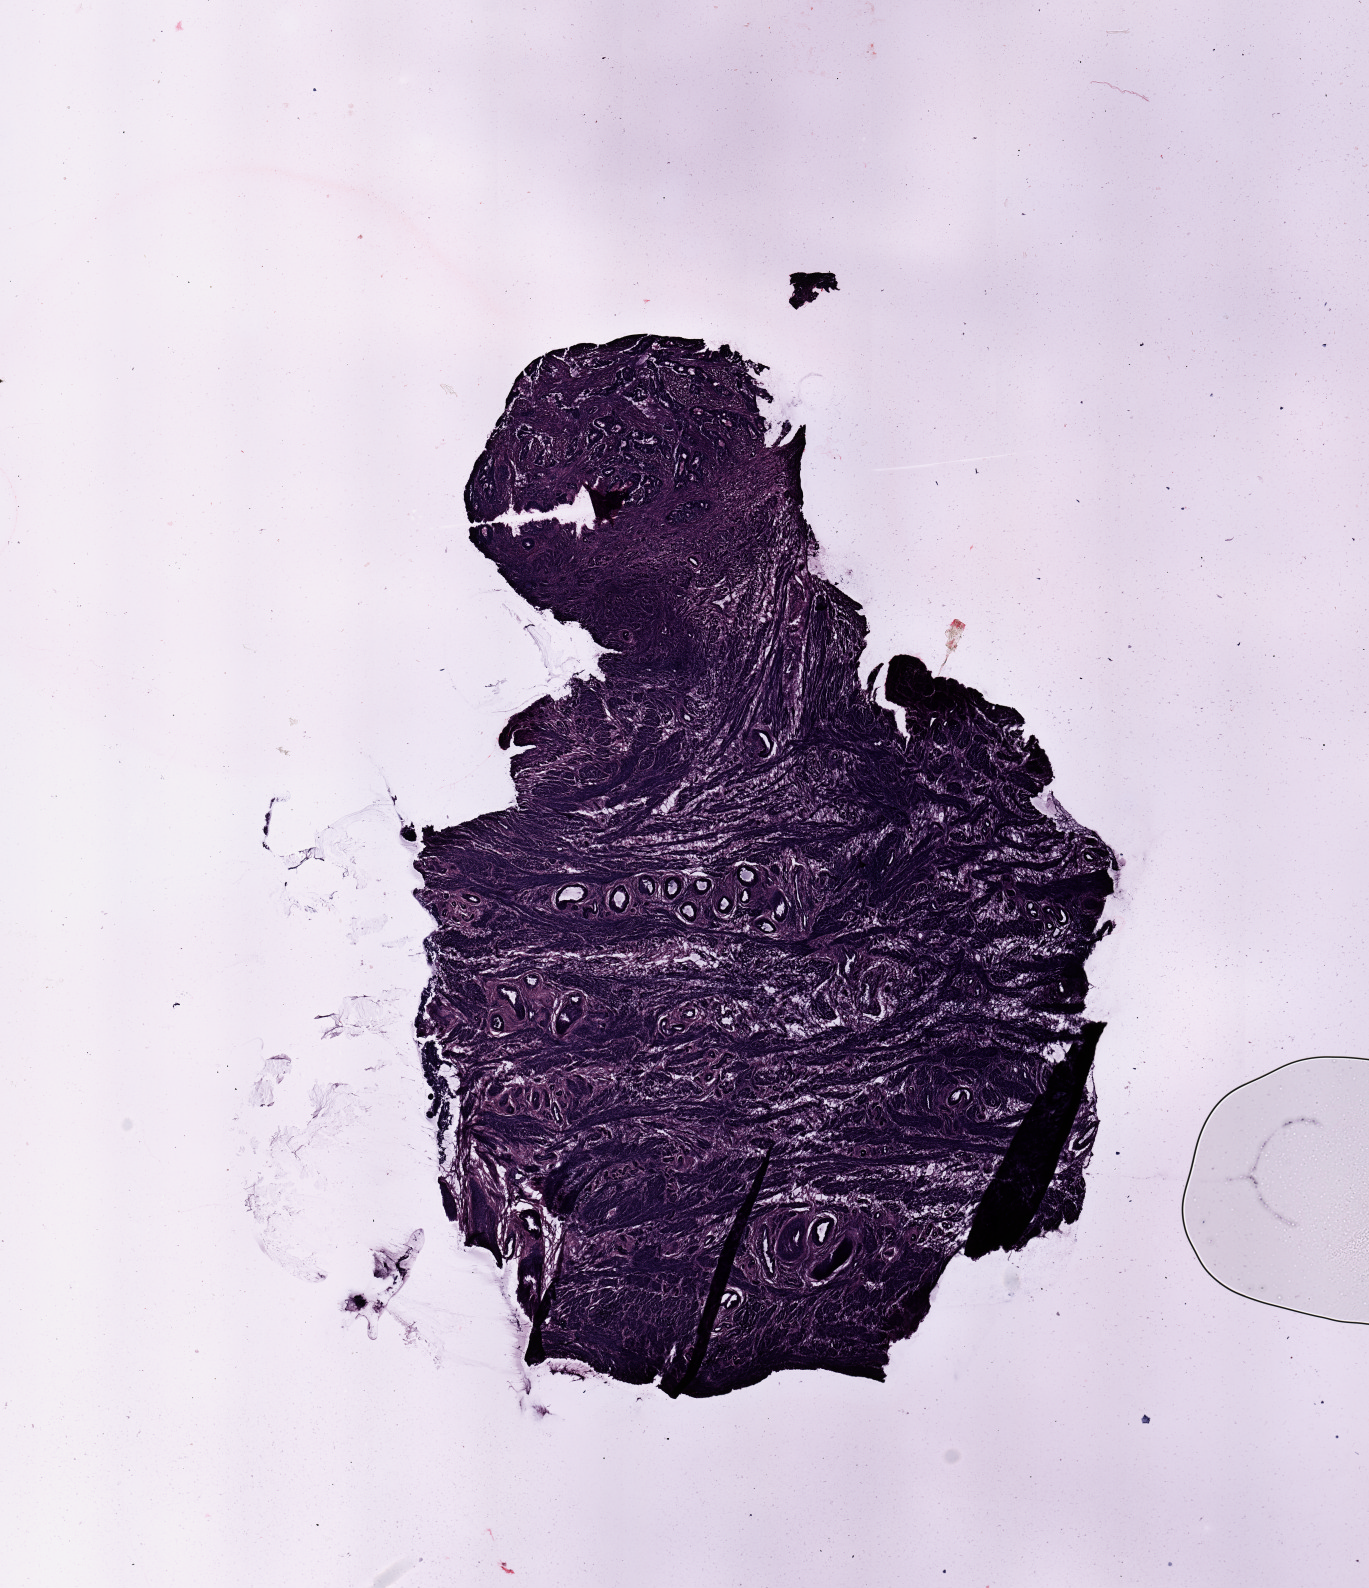
Hematoxylin and eosin (H&E) stained whole-slide image — low-resolution overview of the scanned area, about 10.8 x 12.6 mm, uterus, normal (non-tumour) tissue. Patient: female, age 62 years.
This section: normal (non-tumour) tissue from the same patient. Patient diagnosis: Endometrioid adenocarcinoma, NOS.